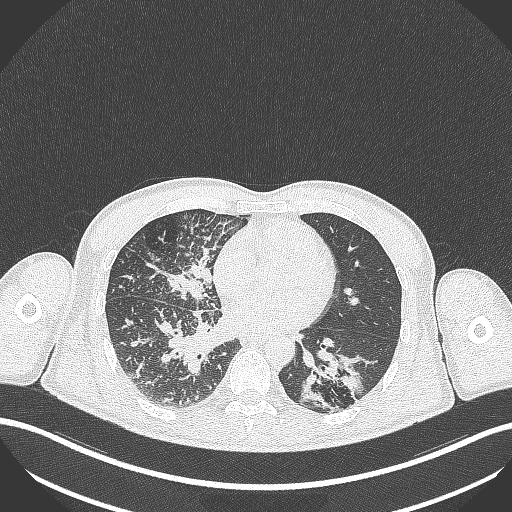
Chest CT, one axial slice; position 134 of 348 along the scan axis; reconstruction kernel B70f; 120 kVp; lung window (W 1500 / L -600 HU); 1 mm slice thickness; 512 × 512 image matrix, field of view 400 × 400 mm. Male patient, age 49 years. From the clinical record (not read from this slice): clinical TNM (as recorded): T2b N1 M0.
Annotated regions visible in this slice (rectangle marked by the reading radiologist):
- lung tumour (recorded histology: adenocarcinoma): bounding box [x1, y1, x2, y2] px = [297, 343, 365, 404]